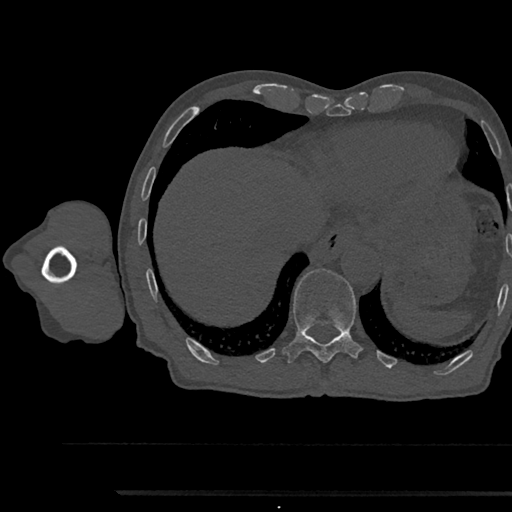
CT including the spine, one axial slice. Position 789 of 797 along the scan axis. Reconstruction kernel Br40s/3. 120 kVp. Bone window (W 1800 / L 400 HU). 0.5 mm slice thickness. 512 × 512 image matrix. Patient: male, 79 years. Case-level facts recorded for this patient, not image findings: primary cancer: prostate.
Annotated regions visible in this slice (semi-automatically segmented with operator editing):
- T11 vertebra: bounding box (x1, y1, x2, y2) in pixels: (283, 269, 361, 364)